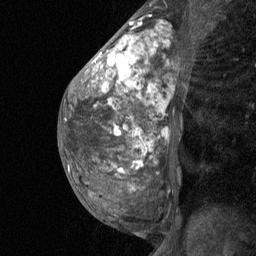
Breast MRI (dynamic contrast-enhanced), one sagittal slice. Position 29 of 64 along the scan axis. Dynamic contrast-enhanced study with each time point stored as its own series, time point 2 of 3 at this slice position (early post-contrast, ordered by acquisition time). 1.5 T. TE 4.8 ms, TR 27 ms. 2 mm slice thickness. 256 × 256 image matrix, field of view 180 × 180 mm. Female patient, age 36 years. From the clinical record (not read from this slice): setting: breast cancer imaged before/during neoadjuvant chemotherapy; receptor status: HR-positive, HER2-negative.
Structures marked on this image (semi-automatic segmentation, software-assisted and operator-edited):
- analysis volume of interest (the breast-tissue region the enhancement analysis was run in; not a lesion): bounding box (x1, y1, x2, y2) in pixels: (67, 12, 194, 238)
- tumour enhancement mask (voxels above the 90 % enhancement threshold inside the analysis volume of interest): (93, 23, 156, 172)